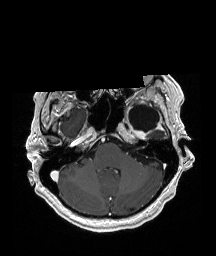
Brain MRI from a brain-tumour surgery series, one axial slice; slice 145 of 192 in the series (ordered by position); T1-weighted post-contrast; 216 × 256 image matrix. Case-level facts recorded for this patient, not image findings: histopathology: Glioblastoma; WHO grade: 4; IDH mutation: no; tumour location: Left Temporal.
Outlined on this slice (expert manual segmentation):
- previous resection cavity: bounding box <129,105,159,132> (left, top, right, bottom; pixels)